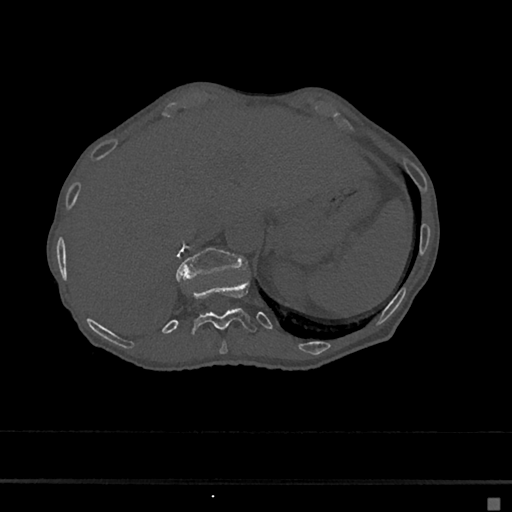
CT including the spine, one axial slice; slice 168 of 797 in the series (ordered by position); bone window (W 1800 / L 400 HU); 0.5 mm slice thickness; 512 × 512 image matrix, field of view 360 × 360 mm. Patient: female, 68 years. Case-level facts recorded for this patient, not image findings: primary cancer: renal.
Annotated regions visible in this slice (semi-automatically segmented with operator editing):
- T10 vertebra: box from (x=219, y=340) to (x=228, y=355) px
- T11 vertebra: (x=188, y=279)–(x=257, y=336)
- T12 vertebra: (x=175, y=247)–(x=241, y=279)